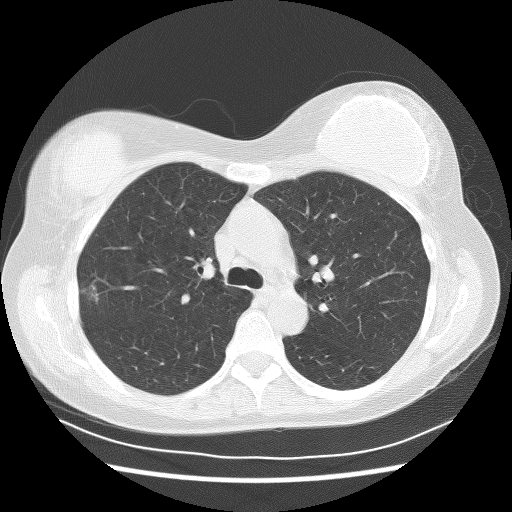
Chest CT (low-dose screening protocol), one axial image, baseline screening round, lung window (W 1500 / L -600 HU), 2.5 mm slice thickness, 512 × 512 image matrix. Female, age 58 years at enrolment. Former smoker at enrolment.
Expert-annotated lung lesion, bounding box [x1, y1, x2, y2] px = [67, 271, 108, 312]. The screening reader recorded 2 non-calcified nodules or masses ≥4 mm on this exam (right upper lobe, right upper lobe); which of them this box marks is not recorded. Official screen result: positive, change unspecified: nodule(s) >= 4 mm or enlarging nodule(s), mass(es), or other non-specific abnormalities suspicious for lung cancer. Lung cancer was diagnosed 510 days after this screen: bronchiolo-alveolar adenocarcinoma, NOS, right upper lobe, well differentiated (G1), stage IA (AJCC 6th edition).